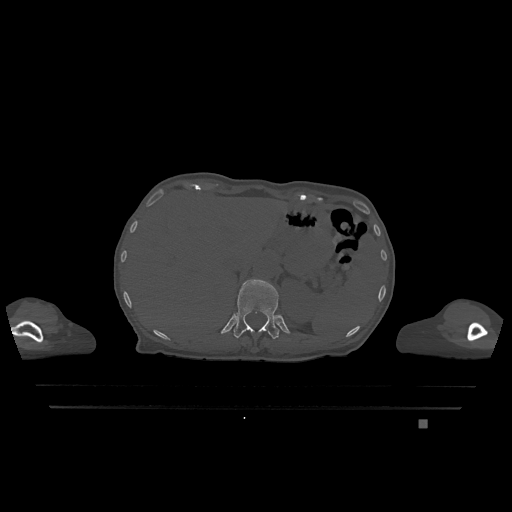
CT including the spine, one axial slice; position 538 of 1317 along the scan axis; bone window (W 1800 / L 400 HU); 0.5 mm slice thickness; 512 × 512 image matrix, field of view 500 × 500 mm. Patient: female, 74 years. From the clinical record (not read from this slice): primary cancer: lung.
Annotated regions visible in this slice (semi-automatically segmented with operator editing):
- T12 vertebra: box from (x=234, y=279) to (x=279, y=339) px